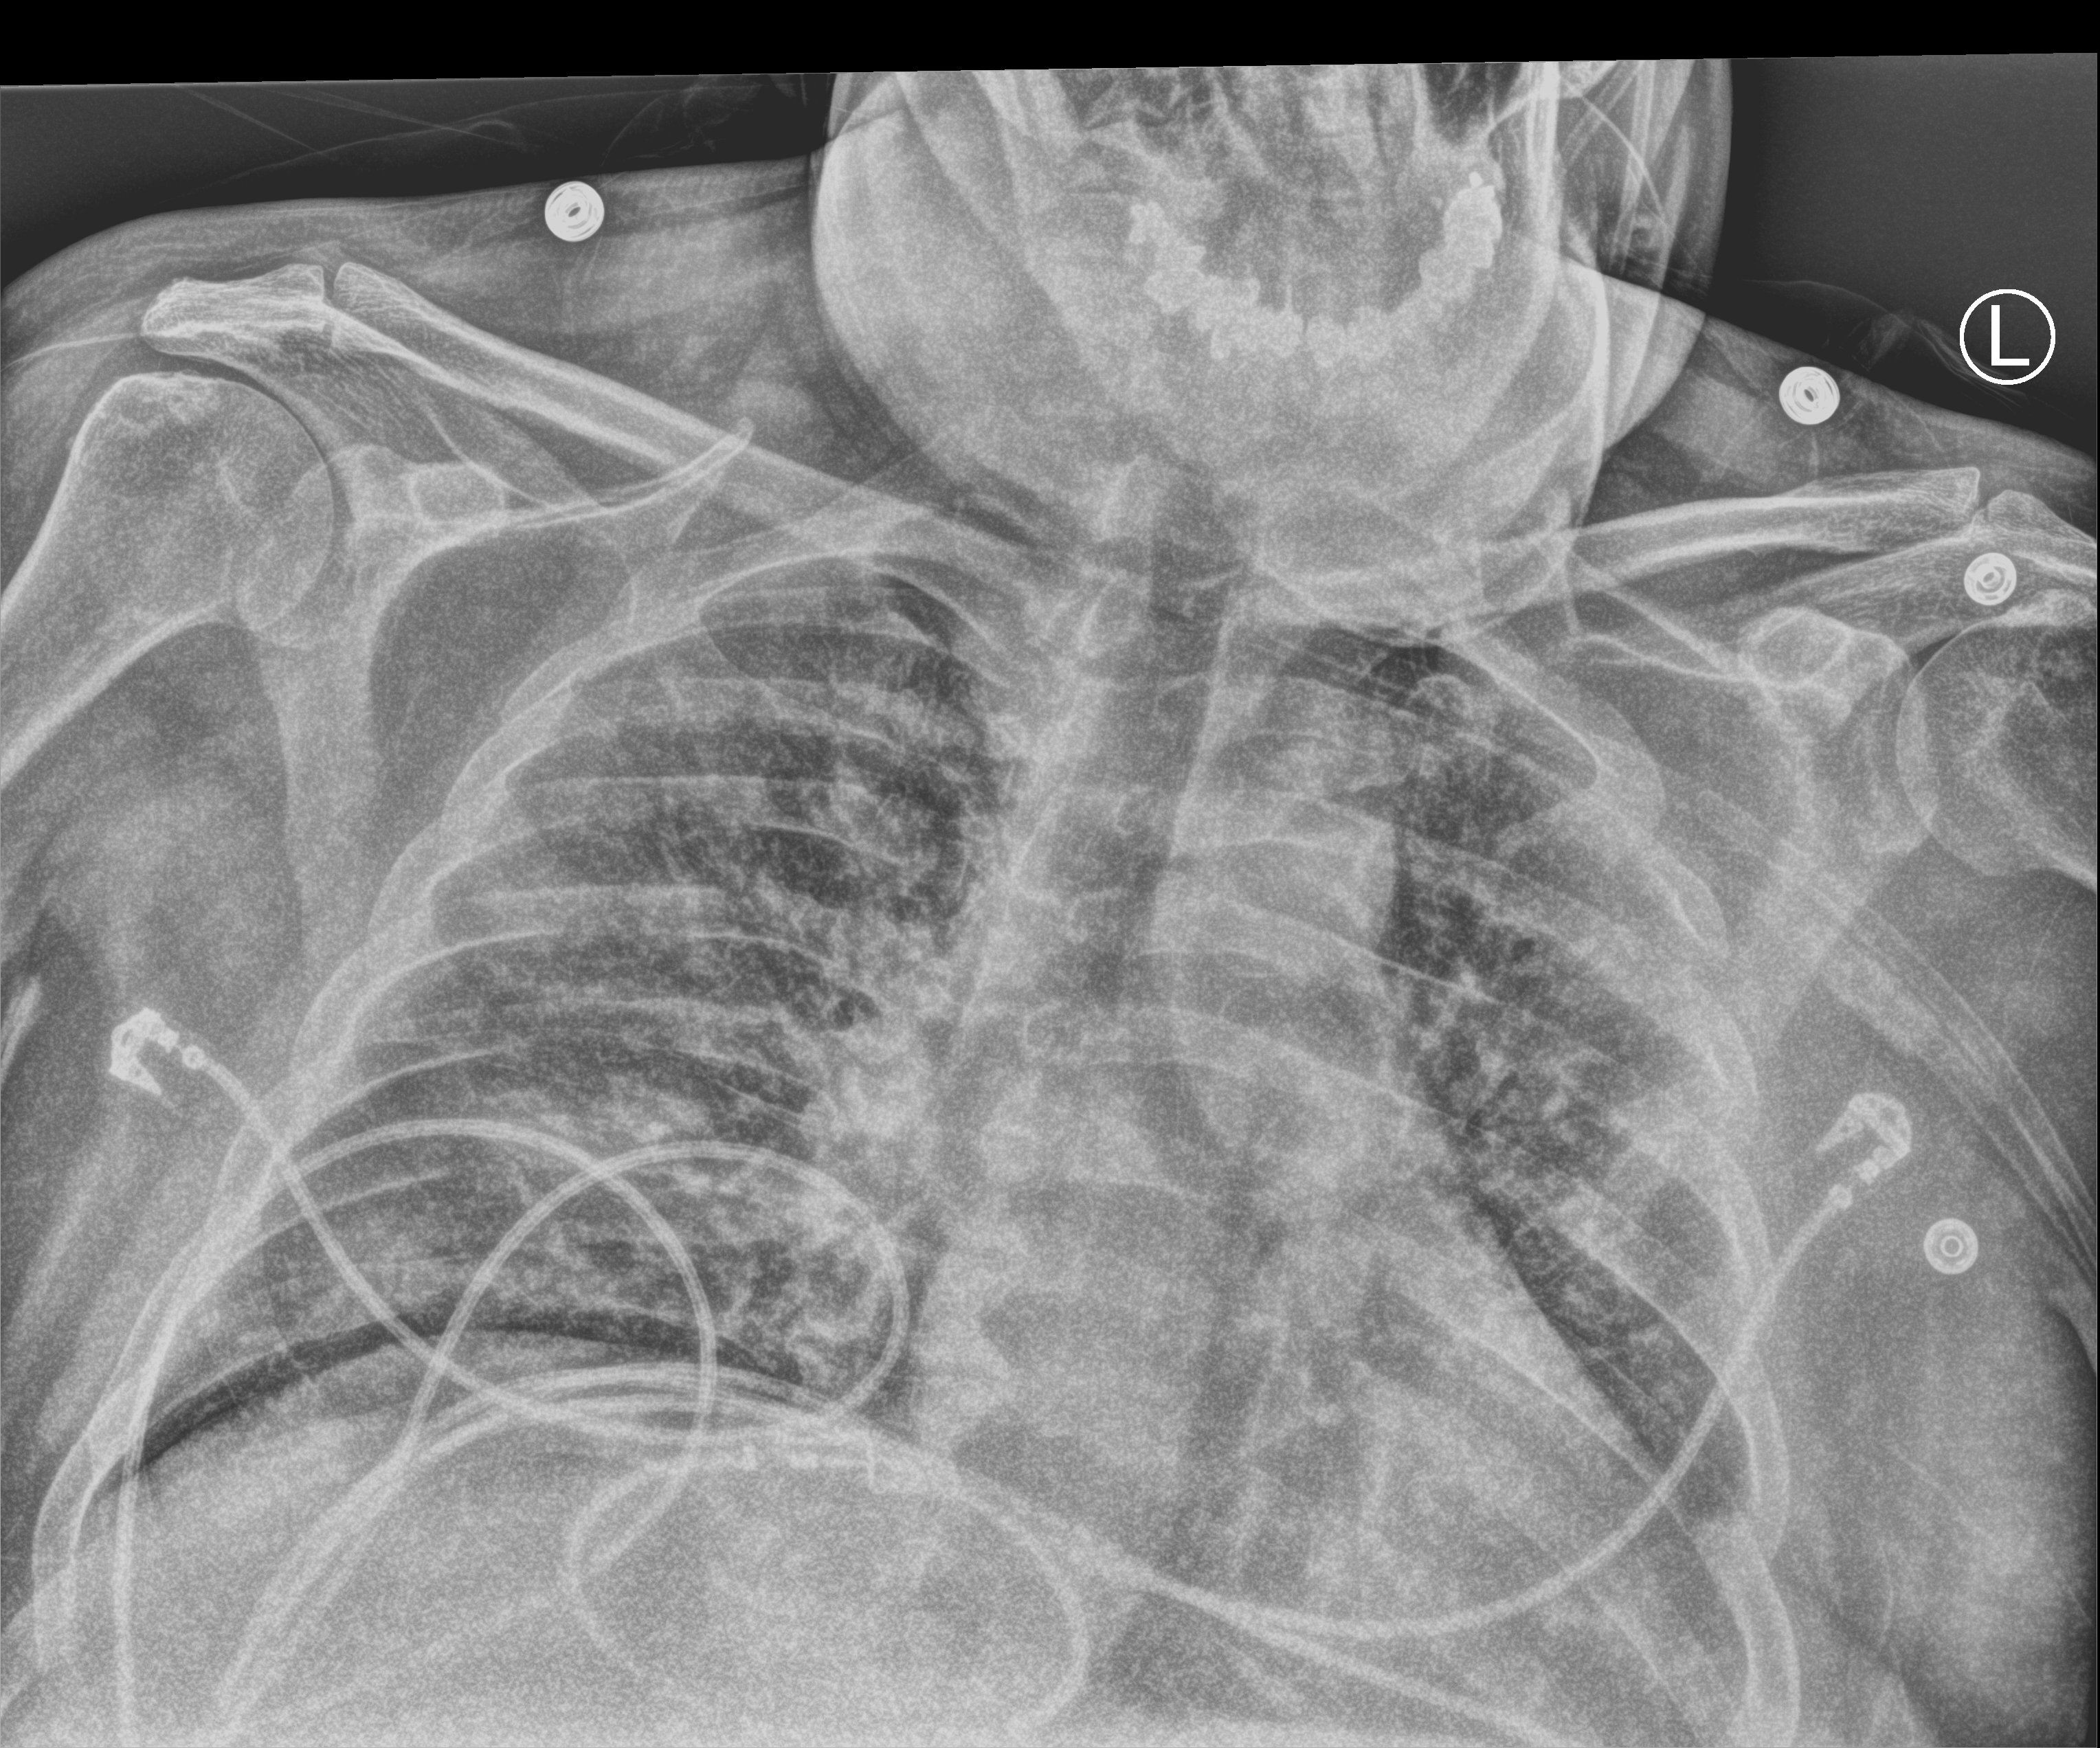
Chest X-ray (portable), anteroposterior (AP) projection. Male patient hospitalised with COVID-19, age 18–59 years.
Hospital-stay facts (about this admission, not read from this image; timing relative to this image not recorded): length of hospital stay: 18 days.